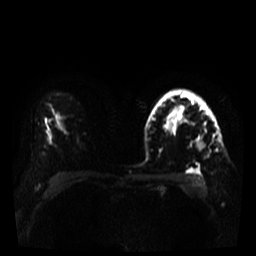
Breast MRI, one axial slice; slice 25 of 35 in the series (ordered by position); diffusion-weighted series; image 2 of 4 stored at this slice position (different b-values; order by instance number); 3 T; 5 mm slice thickness; 256 × 256 image matrix, field of view 320 × 320 mm. Female patient.
Annotated regions visible in this slice (expert manual segmentation):
- tumour on diffusion-weighted imaging: box from (x=175, y=108) to (x=205, y=150) px